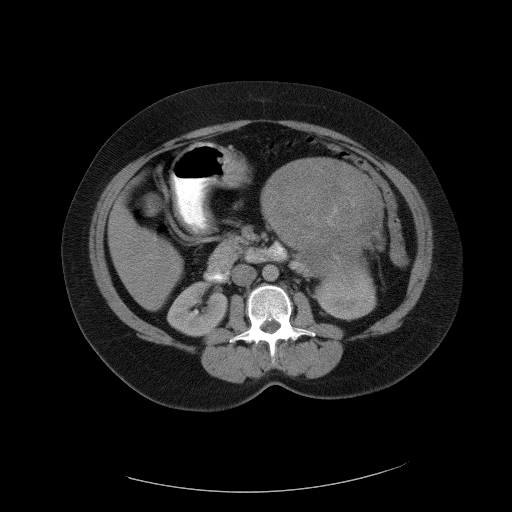
Contrast-enhanced abdominal CT, one axial slice. Slice 57 of 90 in the series (ordered by position). Reconstruction kernel FC01. Intravenous contrast given. Soft-tissue window (W 400 / L 40 HU). 5 mm slice thickness. 512 × 512 image matrix, field of view 480 × 480 mm. Female patient, age 55 years. From the clinical record (not read from this slice): diagnosis: adrenocortical carcinoma; tumour side: left adrenal; tumour size at pathology: 22 cm.
Outlined on this slice (semi-automatically segmented with operator editing):
- mass: bounding box [x1, y1, x2, y2] px = [264, 158, 381, 274]